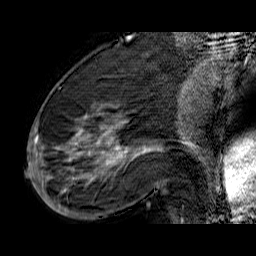
Breast MRI (dynamic contrast-enhanced), one sagittal slice. Position 23 of 60 along the scan axis. Dynamic contrast-enhanced series, time point 2 of 6 at this slice position (early post-contrast). 1.5 T. TE 6.5 ms, TR 32.9 ms. 4 mm slice thickness. 256 × 256 image matrix, field of view 200 × 200 mm. Female patient. Case-level facts recorded for this patient, not image findings: setting: breast cancer imaged before/during neoadjuvant chemotherapy; receptor status: HR-positive, HER2-negative.
Annotated regions visible in this slice (semi-automatically segmented with operator editing):
- analysis volume of interest (the breast-tissue region the enhancement analysis was run in; not a lesion): bounding box <33,74,176,210> (left, top, right, bottom; pixels)
- tumour enhancement mask (voxels above the 100 % enhancement threshold inside the analysis volume of interest): <33,106,150,197>